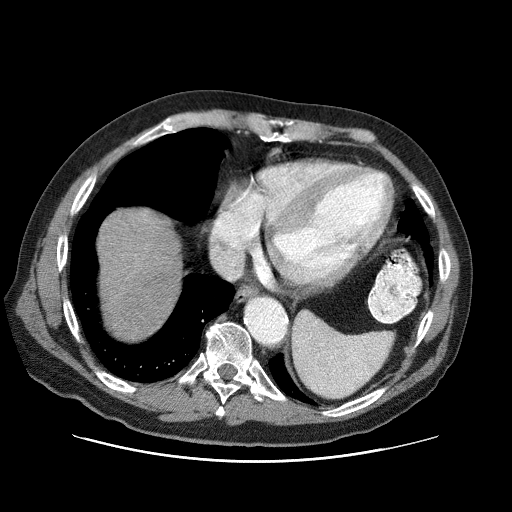
Contrast-enhanced abdominal CT (liver protocol), one axial slice. Position 70 of 87 along the scan axis. One of 3 acquisitions stored at this slice position. Soft-tissue window (W 400 / L 40 HU). 2.5 mm slice thickness. 512 × 512 image matrix. Case-level facts recorded for this patient, not image findings: diagnosis: hepatocellular carcinoma (patient treated with transarterial chemoembolisation; whether this scan precedes or follows treatment is not stated here); TNM stage (as recorded): Stage-IIIA; Child-Pugh class: A; tumour differentiation: well differentiated; tumour nodularity: multinodular.
Annotated regions visible in this slice (semi-automatically segmented with operator editing):
- liver parenchyma outside the tumour (the mass and vessels are separate outlines, so this box may not span the whole liver): bounding box [x1, y1, x2, y2] px = [98, 208, 182, 338]